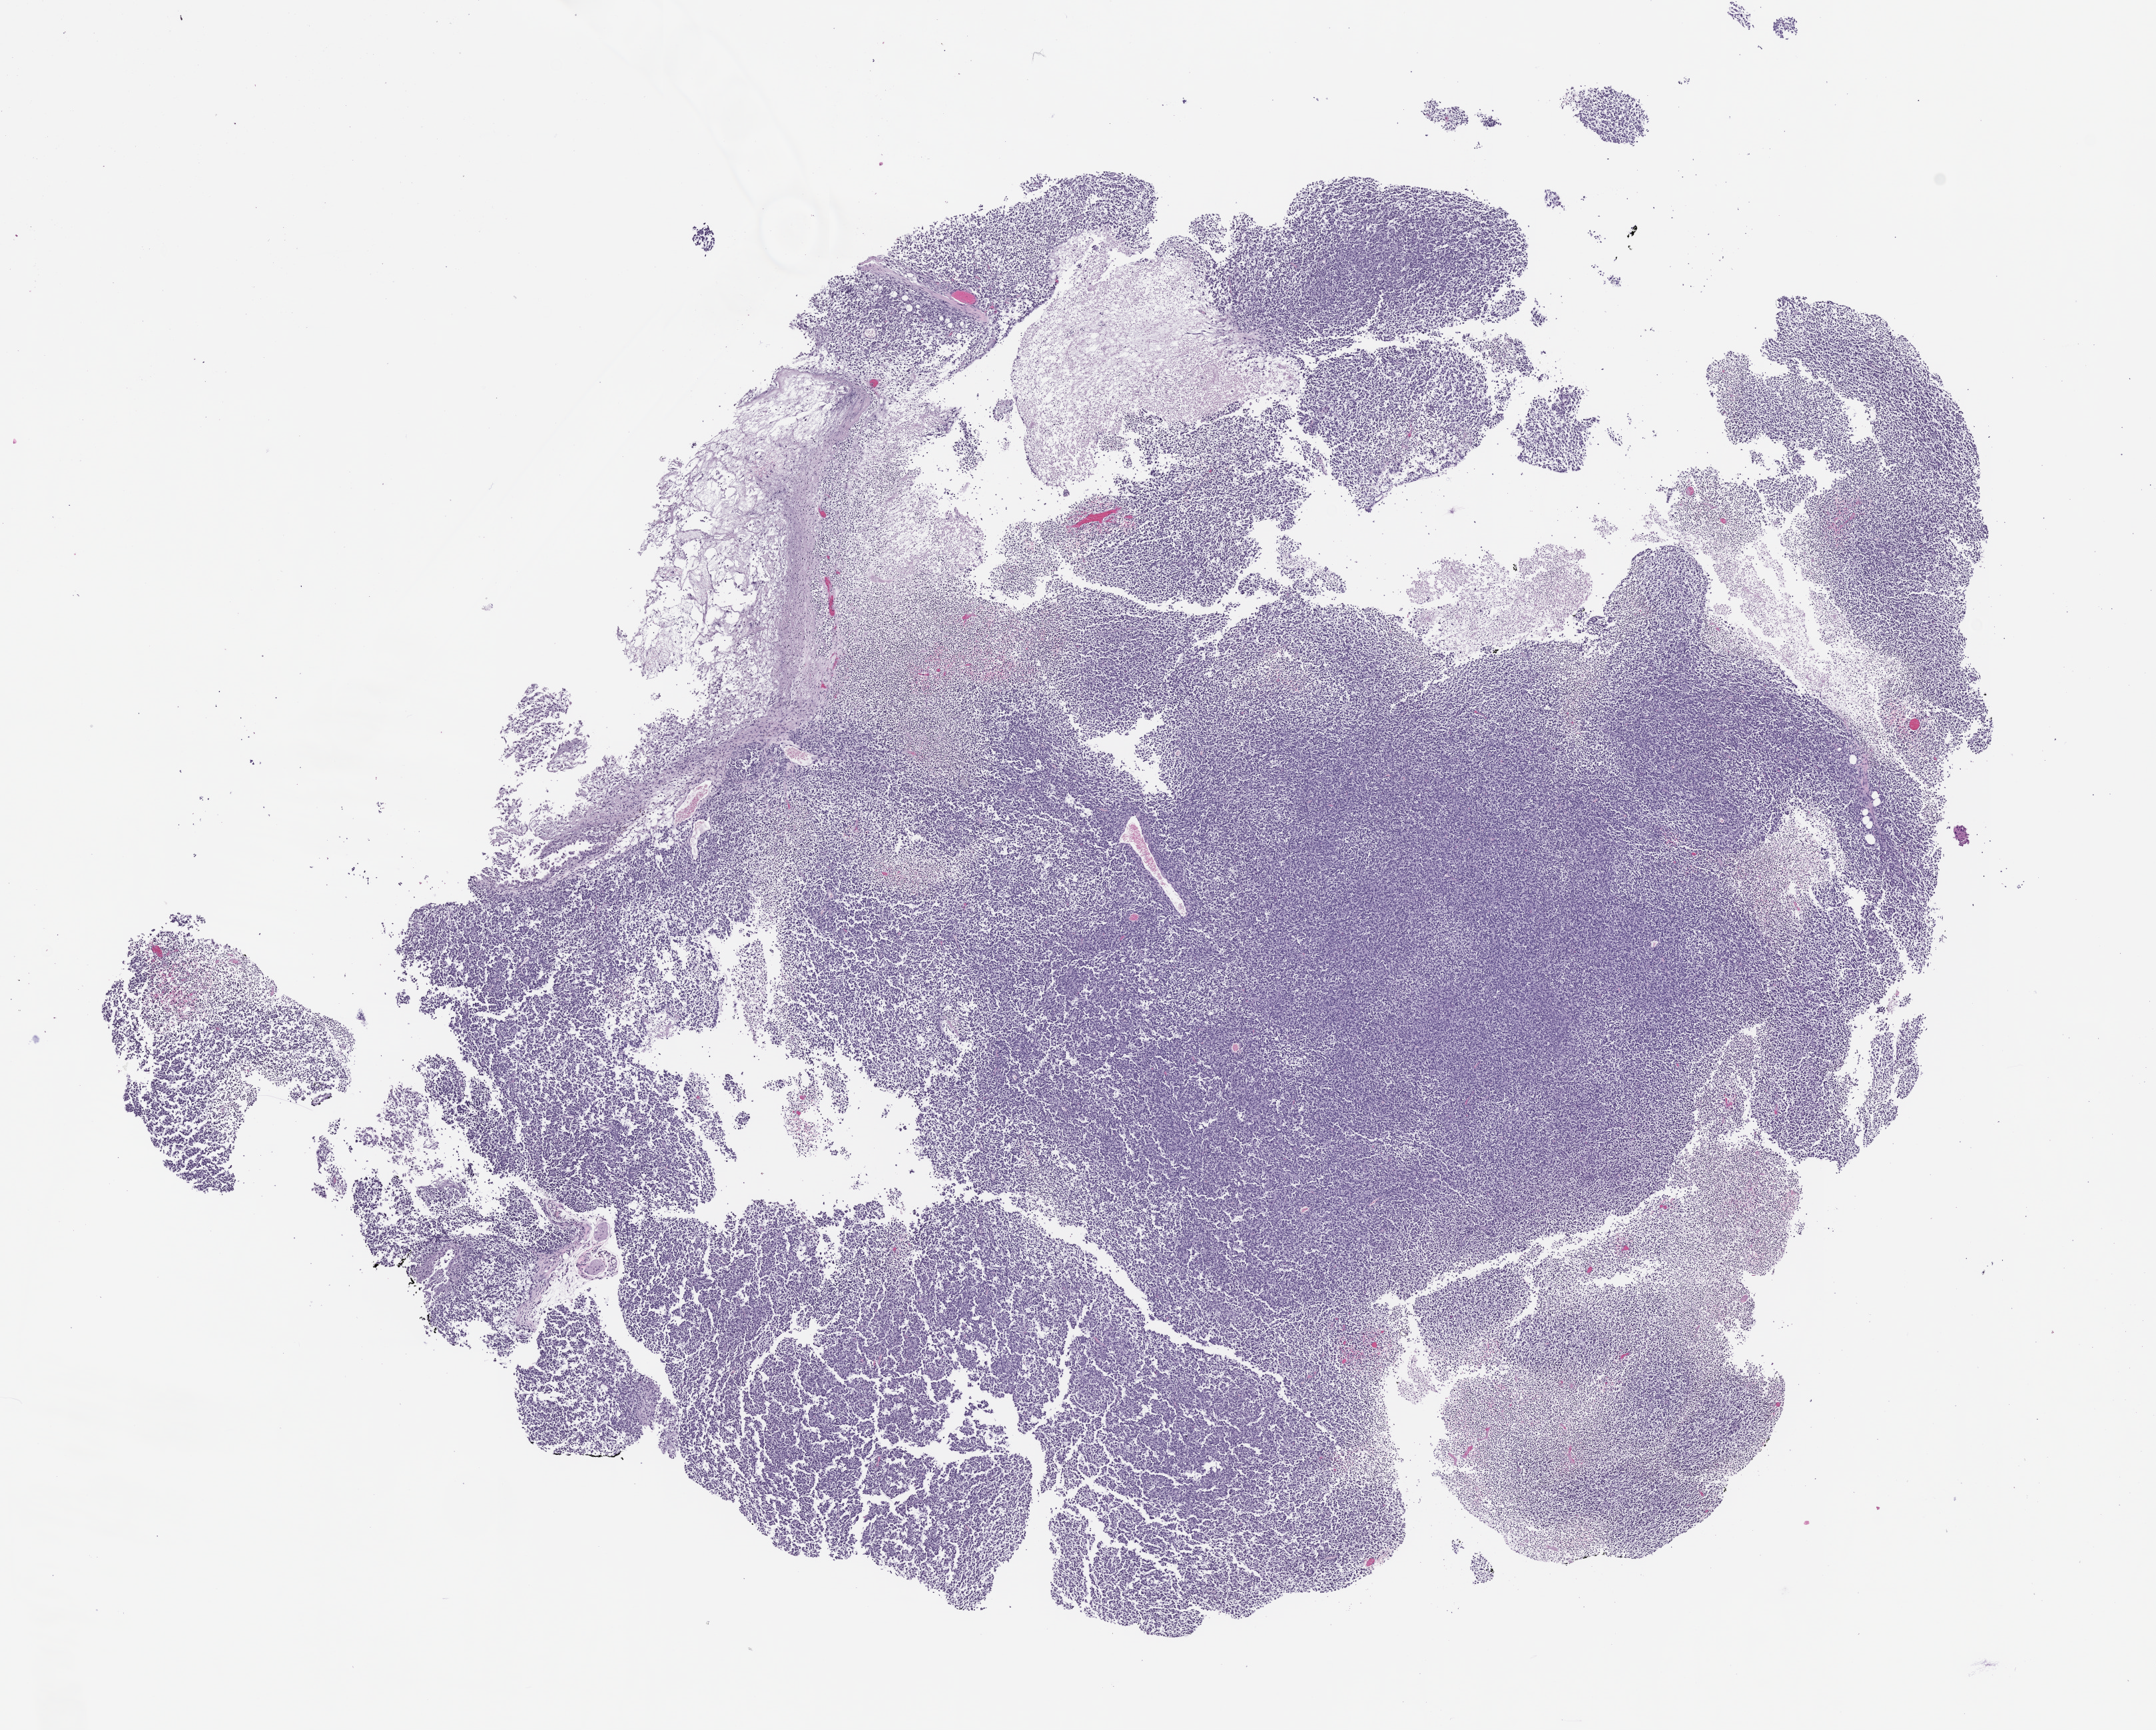
H&E whole-slide image of a patient-derived xenograft (PDX) tumor grown in a mouse, passage 2 — shown as a low-resolution overview of the whole scanned area (about 13.0 x 10.4 mm), formalin-fixed, paraffin-embedded (FFPE) tissue, originating tumor site category: musculoskeletal.
• originating patient diagnosis: Ewing Sarcoma|Primitive Neuroectodermal Tumor